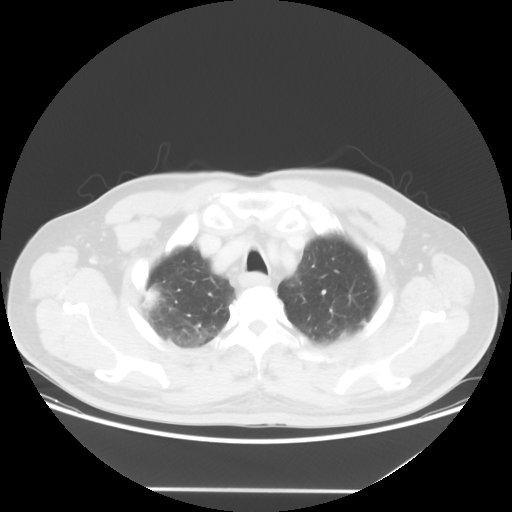
Chest CT, one axial slice; slice 45 of 54 in the series (ordered by position); 120 kVp; lung window (W 1500 / L -600 HU); 5 mm slice thickness; 512 × 512 image matrix. Male patient, age 65 years. Case-level facts recorded for this patient, not image findings: clinical TNM (as recorded): T1c N1 M0.
Annotated regions visible in this slice (bounding box drawn by a radiologist):
- lung tumour (recorded histology: adenocarcinoma): bounding box [x1, y1, x2, y2] px = [139, 280, 167, 315]